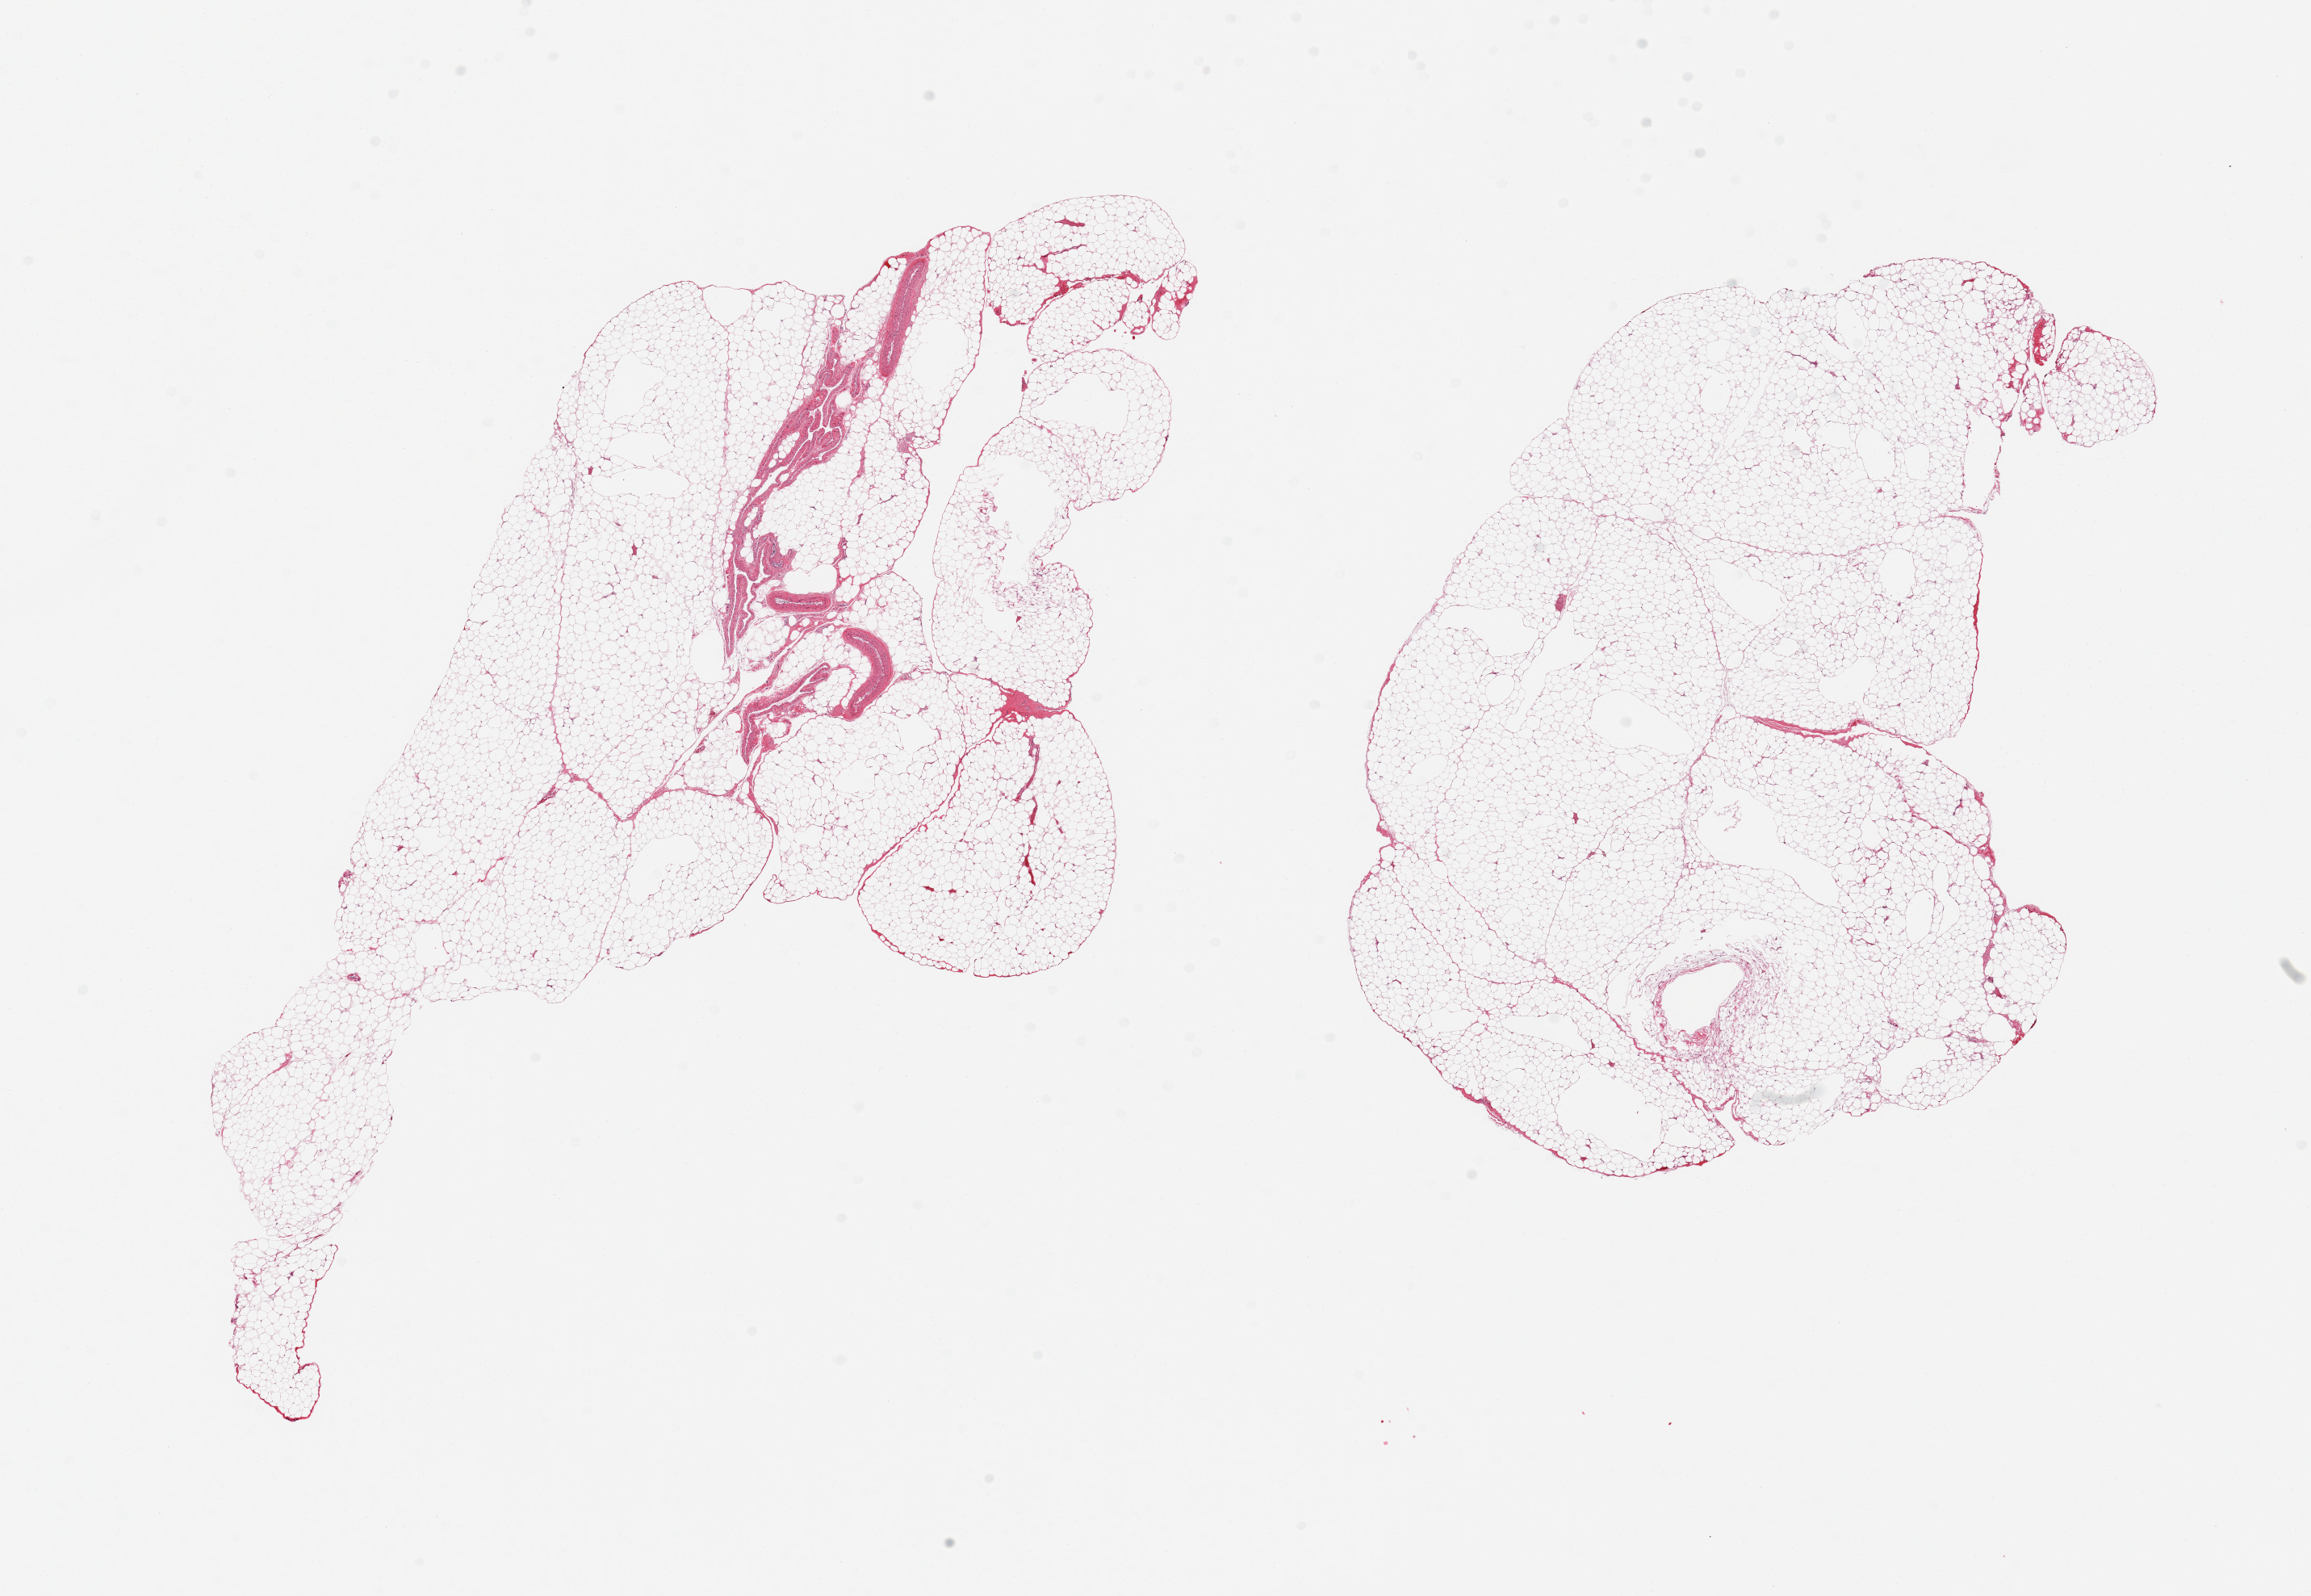
Haematoxylin and eosin whole-slide image, brightfield, low-resolution overview of the scanned area, about 22.6 x 15.6 mm (slide scanned at 20x). PAXgene-fixed paraffin-embedded (PFPE) section. Target tissue: omentum. Tissue donor sample.
Review note (as recorded): 2 pieces, ~10% fascia/vascular elements.